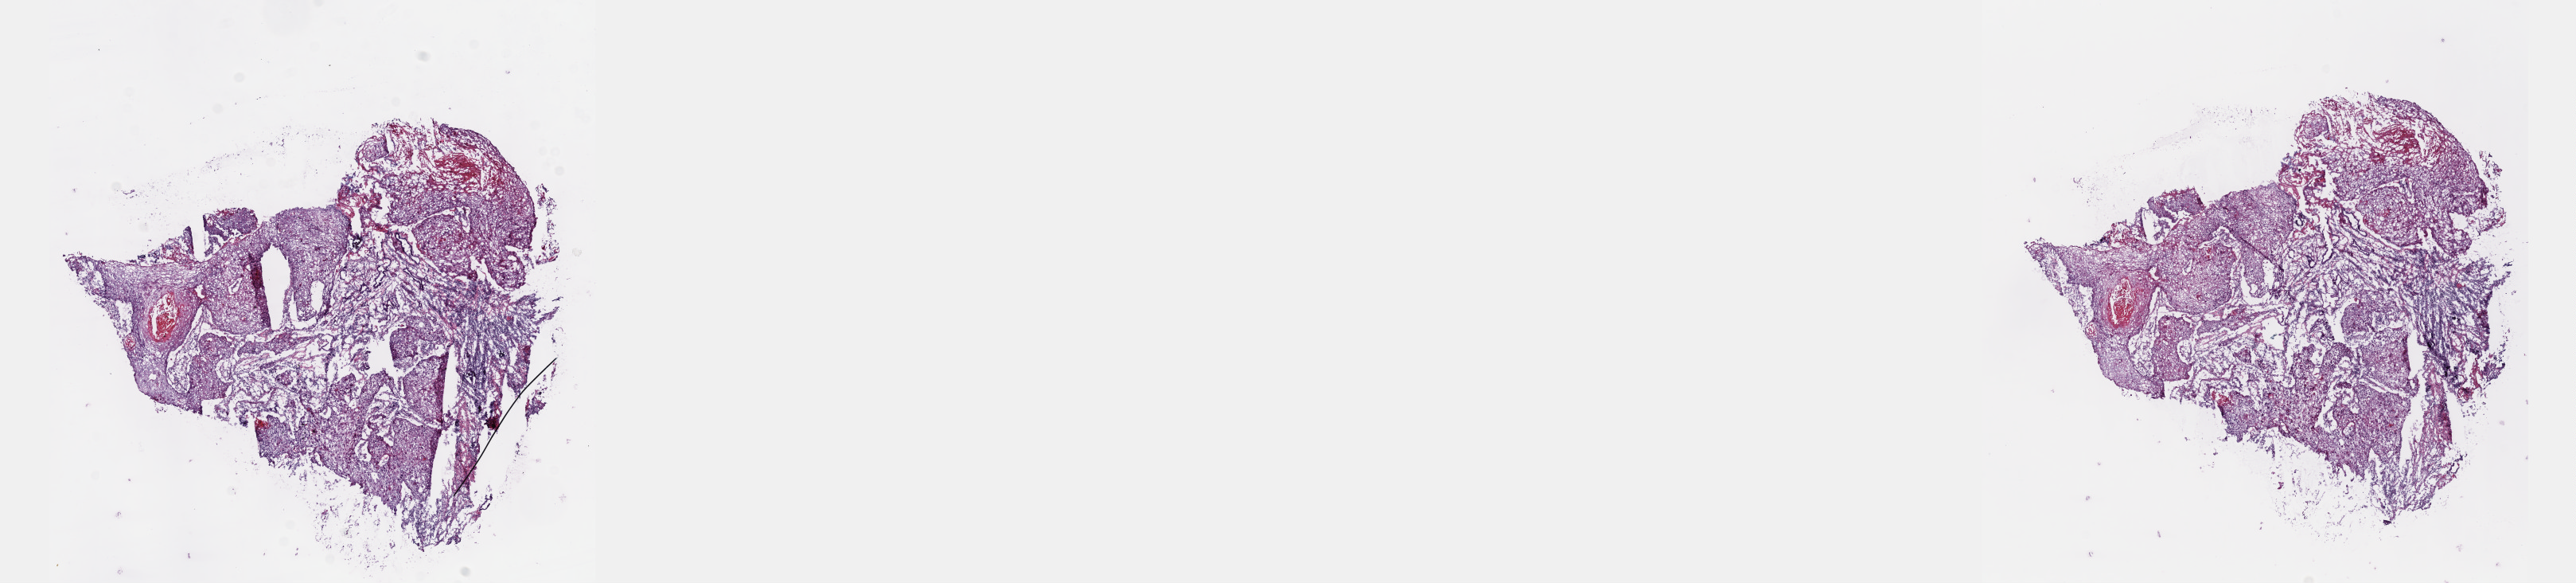
H&E-stained whole-slide image — low-resolution overview of the scanned area, about 26.2 x 5.9 mm (from a 40x scan); frozen section from the top of the tissue portion; esophagus, primary tumour sample. Male patient; age at initial diagnosis 64 years. Histologic grade: G2 (moderately differentiated). Pathologist review of this section (percent, as recorded): tumour cells 50%, tumour nuclei 60%, normal cells 0%, stromal cells 40%, necrosis 10%. Infiltration values recorded for this section: lymphocyte infiltration 40%, monocyte infiltration 0%, neutrophil infiltration 1%.
• diagnosis: Squamous cell carcinoma, NOS (lower third of esophagus)
• lymph nodes positive (case pathology): 0 of 17 examined
• AJCC pathologic stage: IIA (7th edition)